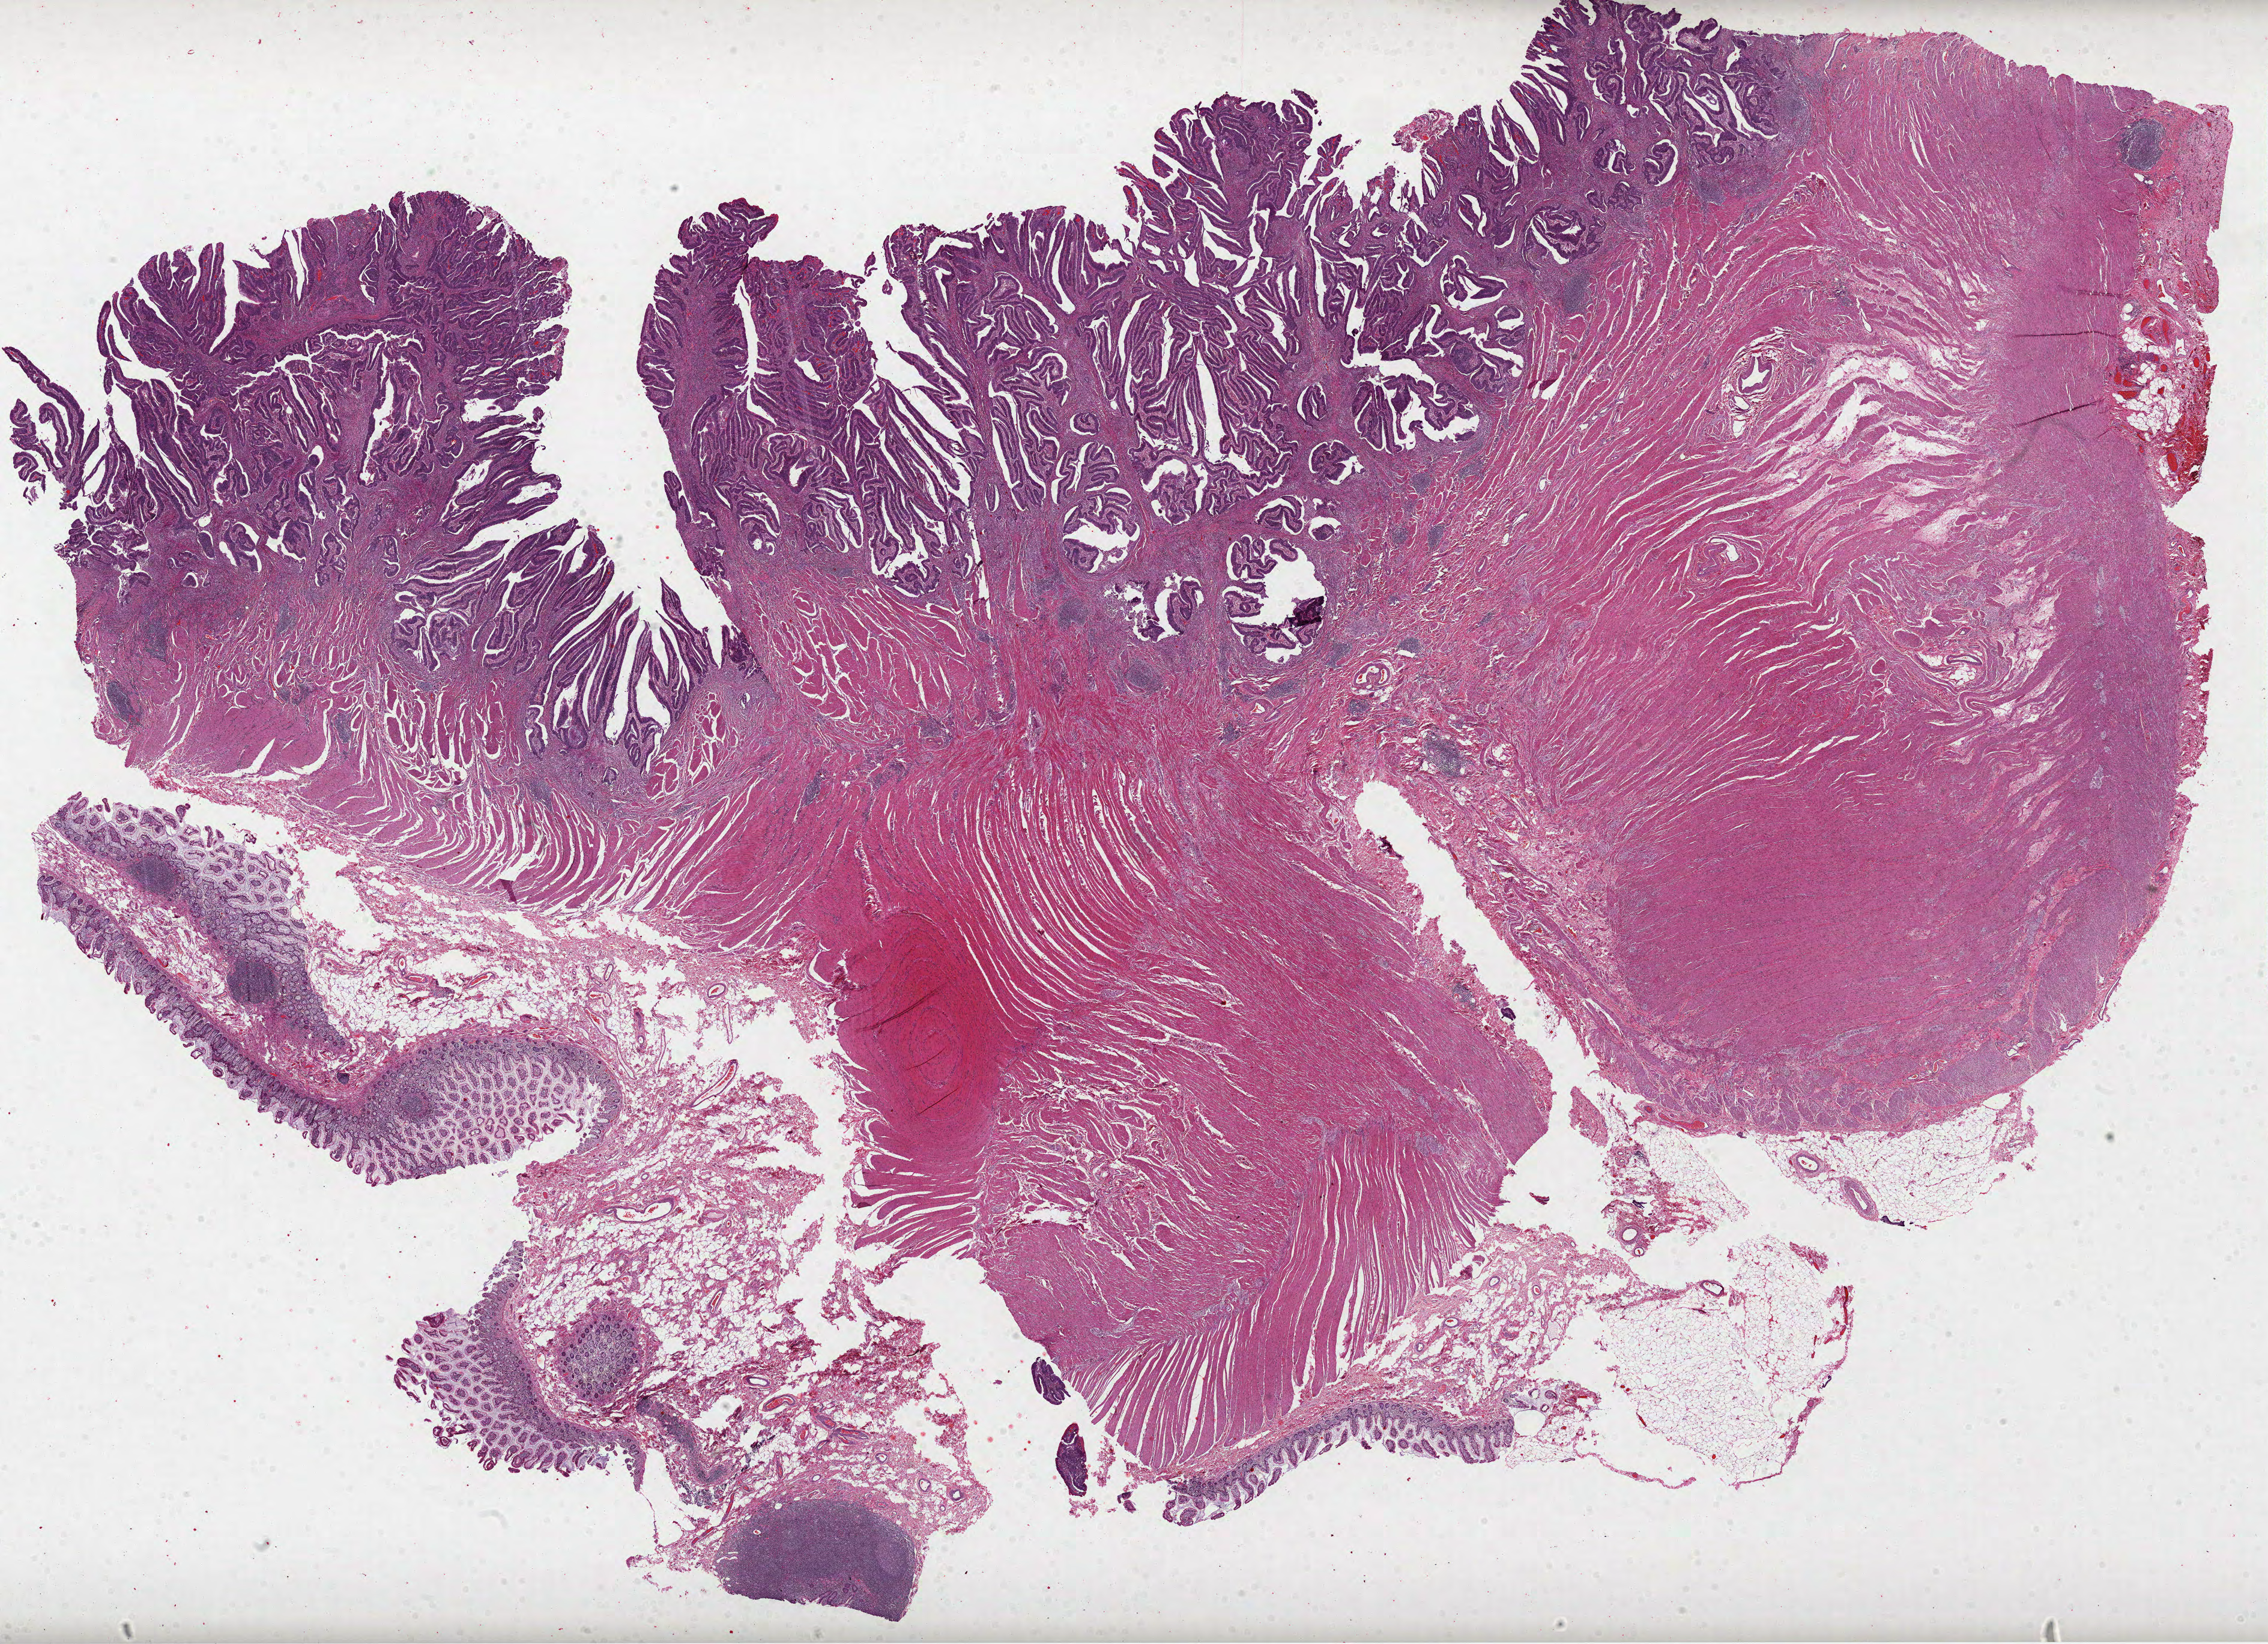
H&E whole-slide image — a low-resolution overview of the entire scanned area, about 30.5 x 22.1 mm (acquisition: 40x scan). Formalin-fixed paraffin-embedded (FFPE) diagnostic section. Primary tumour sample from the colon. Patient: male, age at initial diagnosis 69 years.
Lymph nodes positive (case pathology): 0 of 28 examined. AJCC pathologic stage: I. Histologic diagnosis: Adenocarcinoma, NOS (cecum).